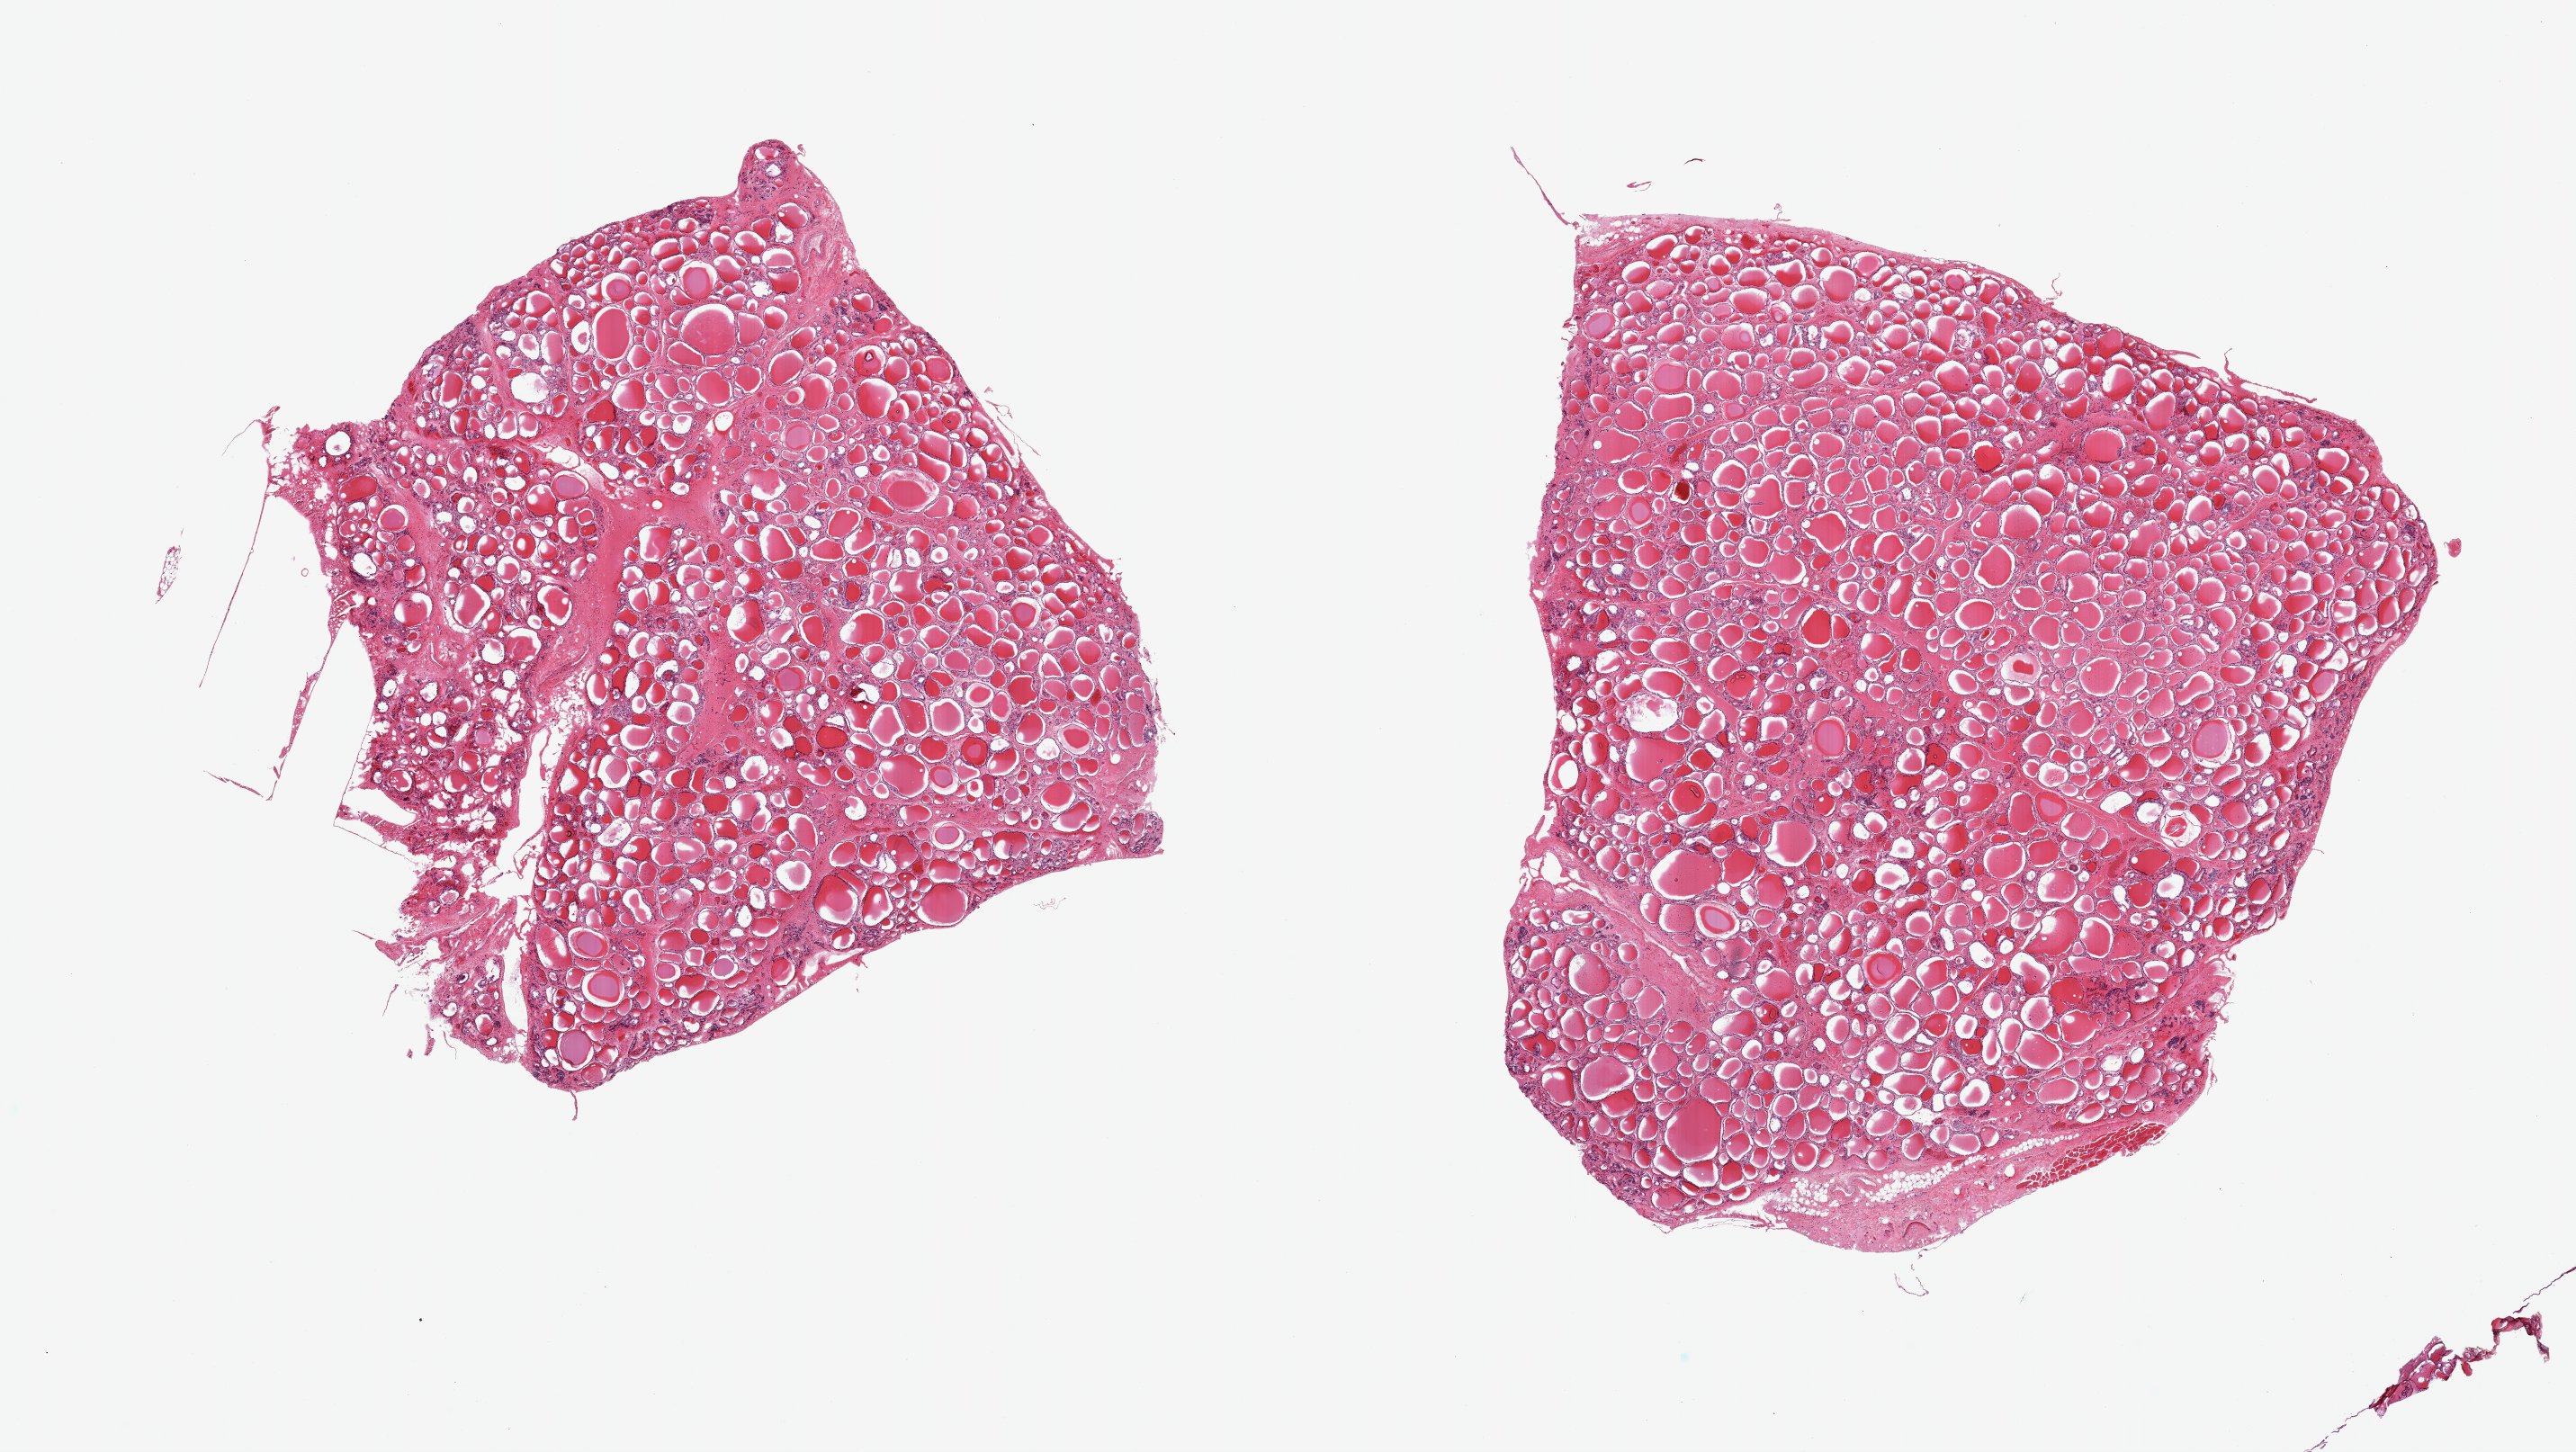
Whole-slide image, haematoxylin and eosin stain — low-resolution overview of the scanned area, about 22.6 x 12.8 mm. PAXgene-fixed paraffin-embedded (PFPE) section. Target tissue: thyroid. Tissue donor sample.
• review note (as recorded): 2 pieces, no significant histopathologic abnormalities